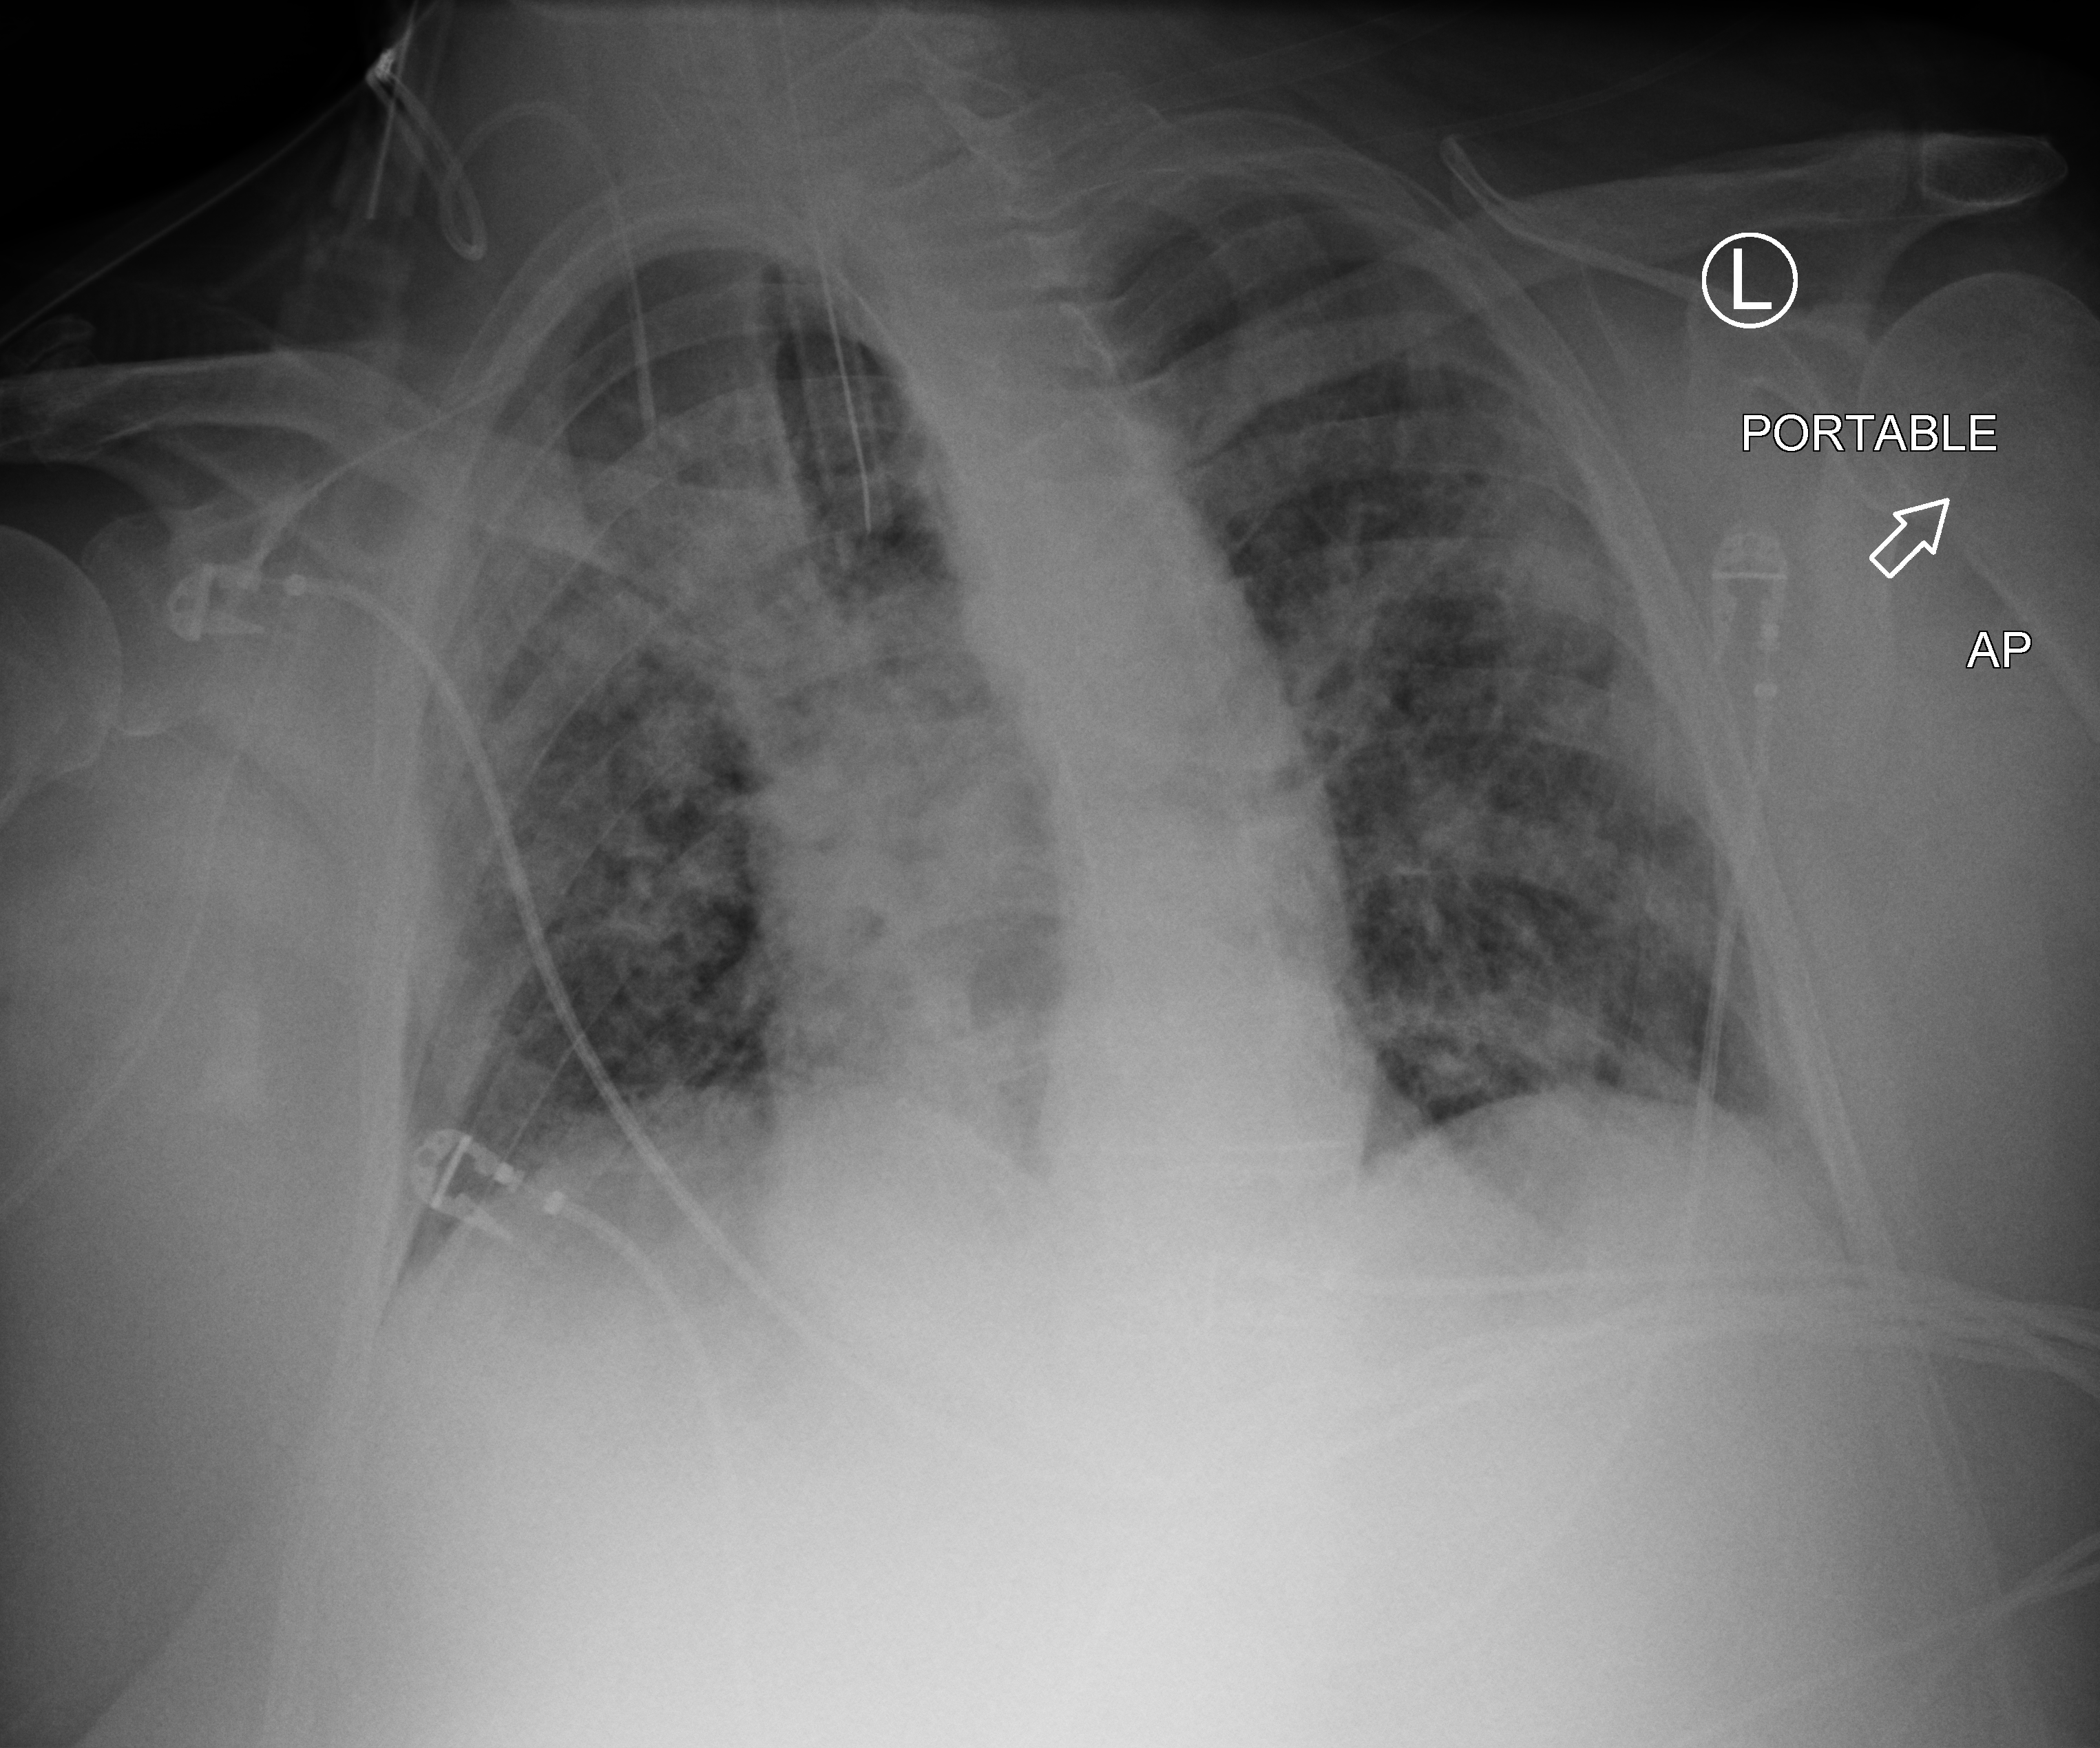
Chest X-ray (portable), anteroposterior (AP) projection. Male patient hospitalised with COVID-19, age 60–74 years.
From the hospital-stay record, not from the radiograph (when in the stay this image was taken is not recorded):
- hypertension (admission record): yes